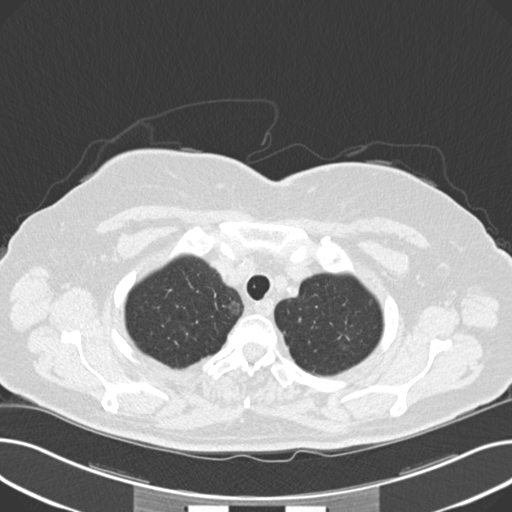
Axial slice from a low-dose chest CT screening exam. Third screening round (two years after baseline). Lung window (W 1500 / L -600 HU). 2 mm slice thickness. Standard (soft-tissue) reconstruction kernel (B30f). 120 kVp. Slice 34 of 203 in the series. 512 × 512 image matrix. Female participant, aged 60 years at enrolment. Current smoker at enrolment.
• Lesion marked by an expert reader, bounding box (x1, y1, x2, y2) in pixels: (338, 321, 381, 367).
• The screening reader recorded 8 non-calcified nodules or masses ≥4 mm on this exam (right upper lobe, lingula, lingula, right middle lobe, right lower lobe, left lower lobe, left lower lobe, left lower lobe); which of them this box marks is not recorded.
• Lung cancer was diagnosed 176 days after this screen: non-small cell carcinoma, left upper lobe, poorly differentiated (G3), stage IB (AJCC 6th edition), 7 mm at pathology.